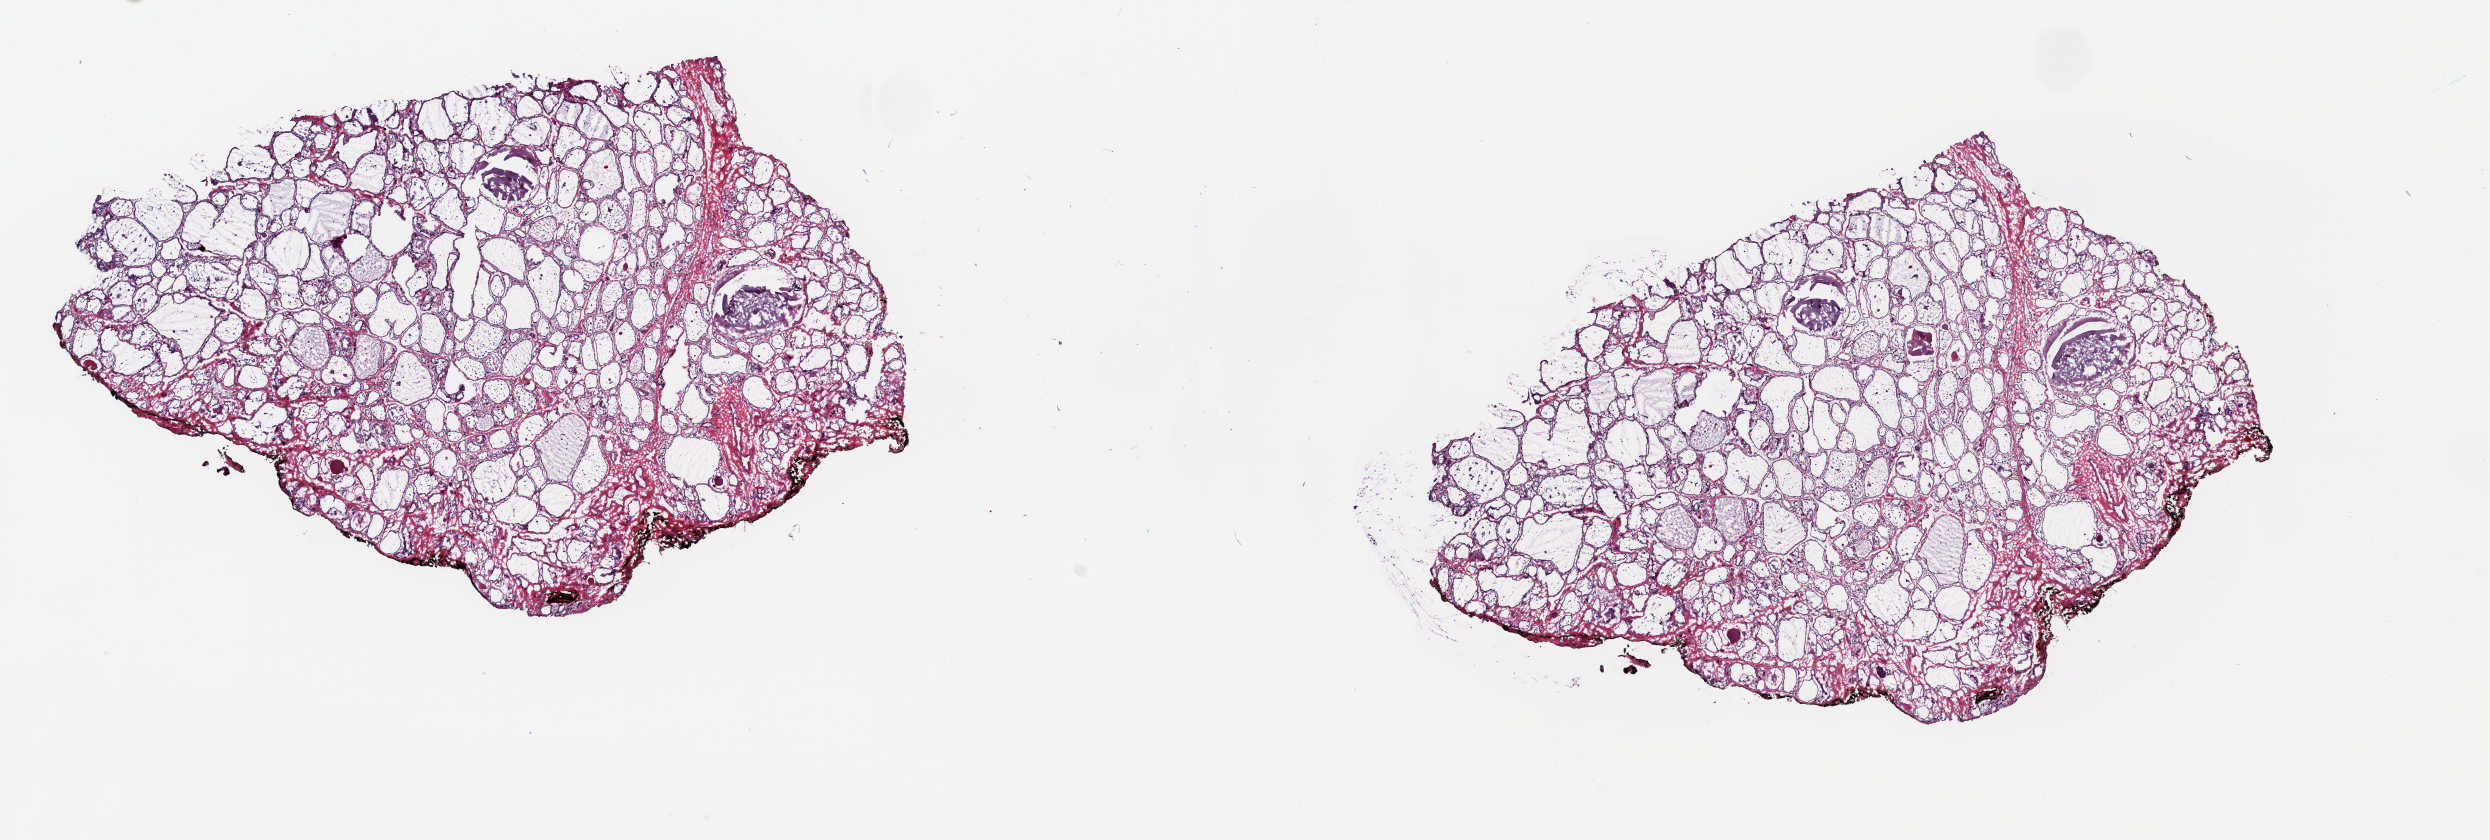
Digitized H&E tissue section (whole slide) — a low-resolution overview of the entire scanned area, about 19.7 x 6.6 mm; frozen section; thyroid, solid tissue normal (non-tumour tissue) sample. Patient: female, age at initial diagnosis 61 years. Slide review estimates, as recorded: tumour cells 0%, tumour nuclei 0%, normal cells 80%, stromal cells 20%, necrosis 0%. Infiltration values recorded for this section: lymphocyte infiltration 2%, monocyte infiltration 1%, neutrophil infiltration 1%.
This section: solid tissue normal sample (biorepository sample class). Patient diagnosis: Papillary adenocarcinoma, NOS (thyroid gland).